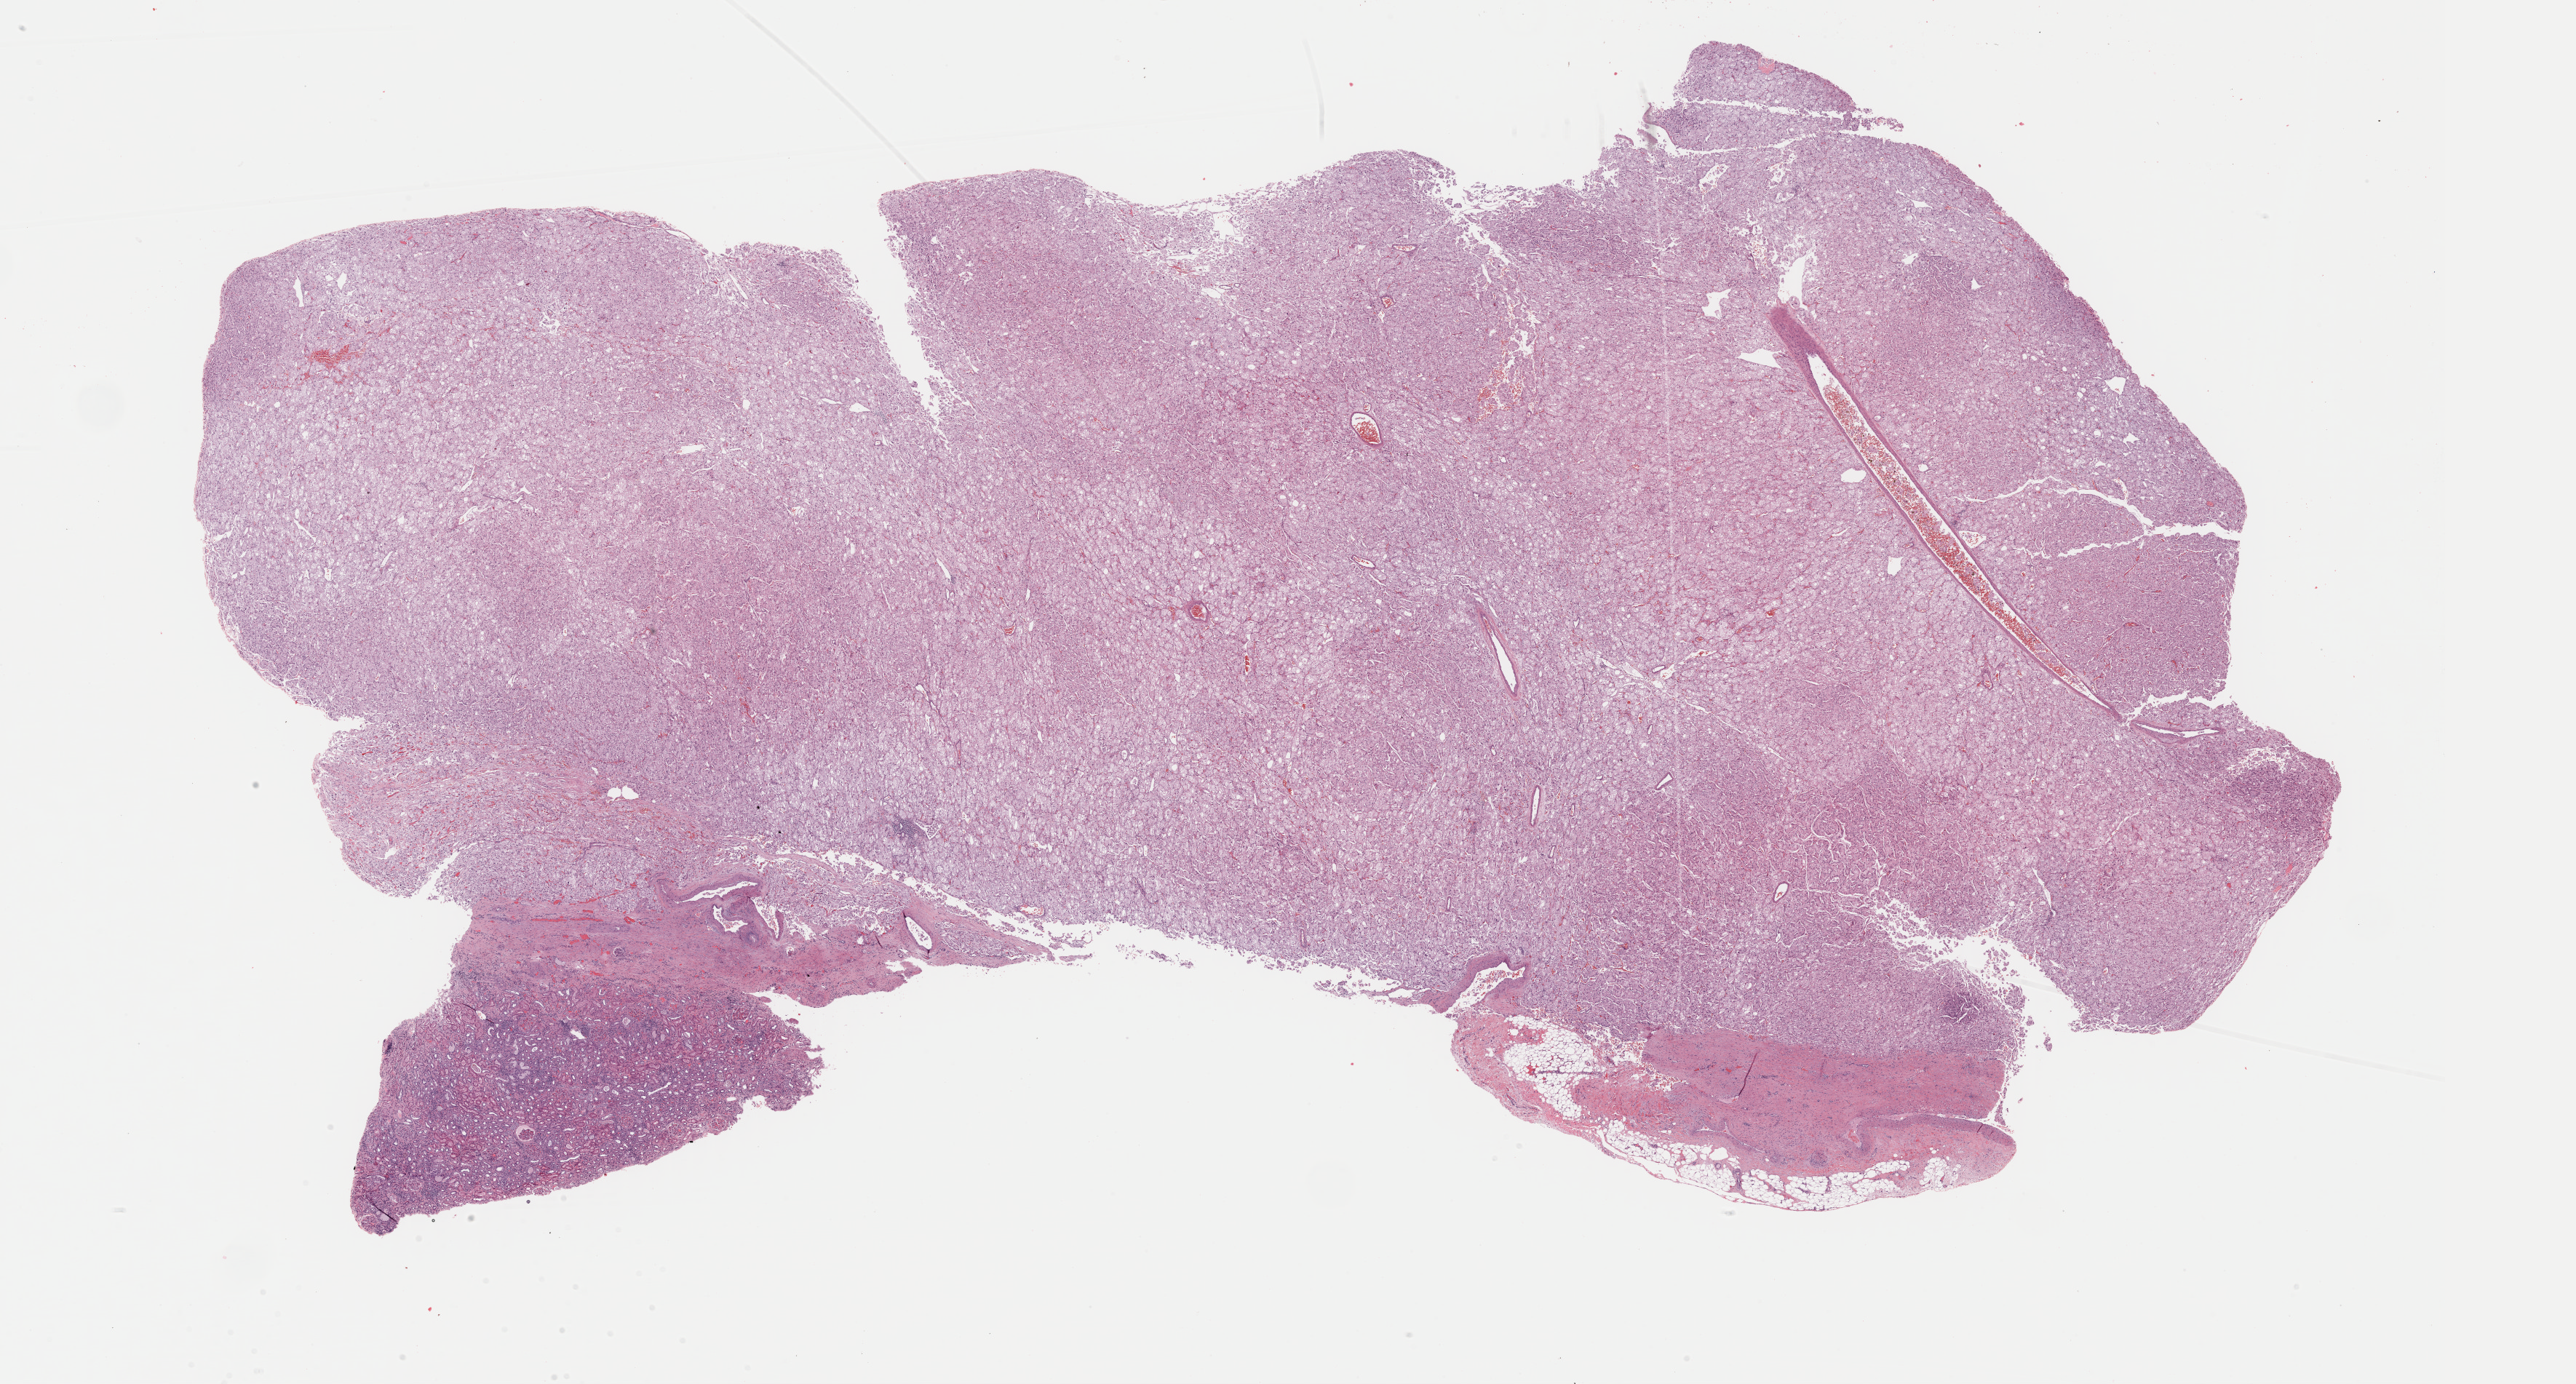
Digitized H&E tissue section (whole slide) — a low-resolution overview of the entire scanned area, about 27.9 x 15.0 mm (from a 40x scan); formalin-fixed paraffin-embedded (FFPE) diagnostic section; kidney, primary tumour sample. Male patient; age at initial diagnosis 46 years.
- AJCC pathologic stage: I
- histologic diagnosis: Renal cell carcinoma, chromophobe type